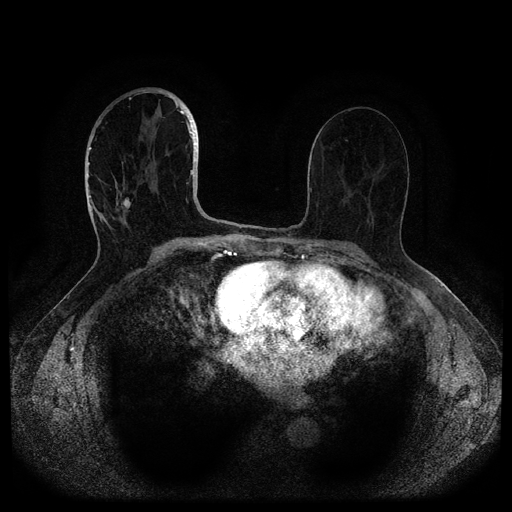
Breast MRI (dynamic contrast-enhanced, multi-phase), one axial slice. Slice 52 of 116 in the series (ordered by position). Dynamic contrast-enhanced series, time point 2 of 5 at this slice position (early post-contrast). 1.5 T. TE 2.6 ms, TR 5.3 ms. 512 × 512 image matrix, field of view 350 × 350 mm. Patient: female, 82 years.
Outlined on this slice (semi-automatically segmented with operator editing):
- breast lesion (labelled 'tumour' in the annotation; benign lesions carry a separate 'benign' label): bounding box (x1, y1, x2, y2) in pixels: (121, 197, 131, 211)